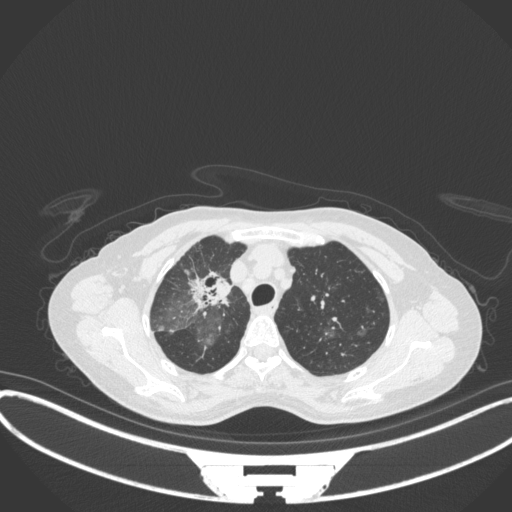
Chest CT, one axial slice; position 250 of 311 along the scan axis; 120 kVp; lung window (W 1500 / L -600 HU); 1 mm slice thickness; 512 × 512 image matrix, field of view 400 × 400 mm. Female patient, age 59 years. Case-level facts recorded for this patient, not image findings: clinical TNM (as recorded): T3 N0 M0; histopathological grade: G1.
Structures marked on this image (bounding box drawn by a radiologist):
- lung tumour (recorded histology: adenocarcinoma): bounding box (x1, y1, x2, y2) in pixels: (188, 268, 237, 316)